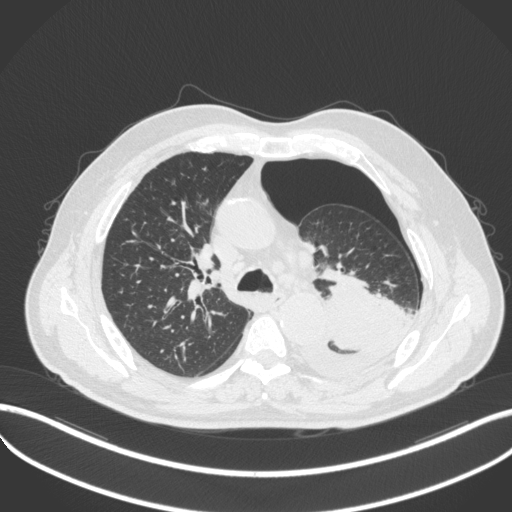
Chest CT, one axial slice; position 344 of 466 along the scan axis; reconstruction kernel B31f; 120 kVp; lung window (W 1500 / L -600 HU); 1 mm slice thickness; 512 × 512 image matrix, field of view 400 × 400 mm. Patient: male, 76 years. From the clinical record (not read from this slice): clinical TNM (as recorded): T3 N0 M1b.
Outlined on this slice (bounding box drawn by a radiologist):
- lung tumour (recorded histology: adenocarcinoma): bounding box [x1, y1, x2, y2] px = [304, 275, 412, 376]